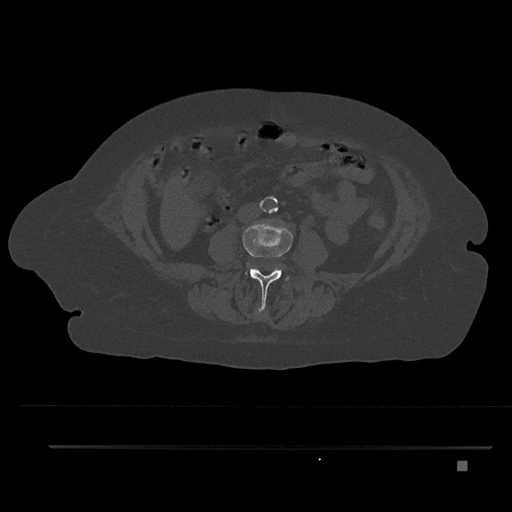
CT including the spine, one axial slice. Slice 119 of 797 in the series (ordered by position). Reconstruction kernel Br40s/3. Bone window (W 1800 / L 400 HU). 0.5 mm slice thickness. 512 × 512 image matrix, field of view 437 × 437 mm. Patient: female, 76 years. From the clinical record (not read from this slice): primary cancer: lung.
Structures marked on this image (semi-automatic segmentation, software-assisted and operator-edited):
- L2 vertebra: box from (x=256, y=307) to (x=264, y=315) px
- L3 vertebra: (x=243, y=220)–(x=293, y=307)
- L4 vertebra: (x=287, y=277)–(x=289, y=279)